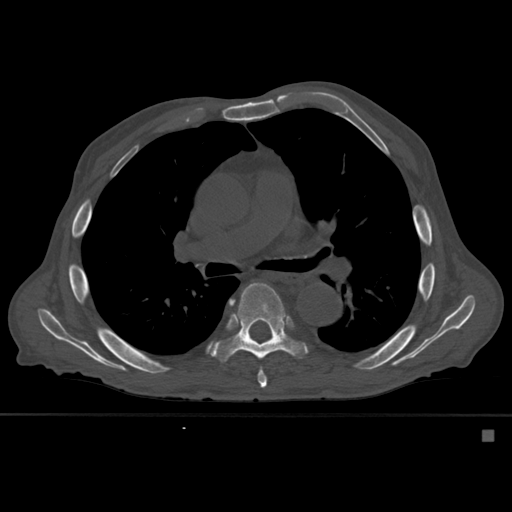
CT including the spine, one axial slice; position 371 of 527 along the scan axis; bone window (W 1800 / L 400 HU); 512 × 512 image matrix. Patient: male, 78 years. Case-level facts recorded for this patient, not image findings: primary cancer: prostate.
Outlined on this slice (semi-automatically segmented with operator editing):
- T6 vertebra: bounding box [x1, y1, x2, y2] px = [232, 300, 267, 388]
- T7 vertebra: [210, 283, 308, 362]